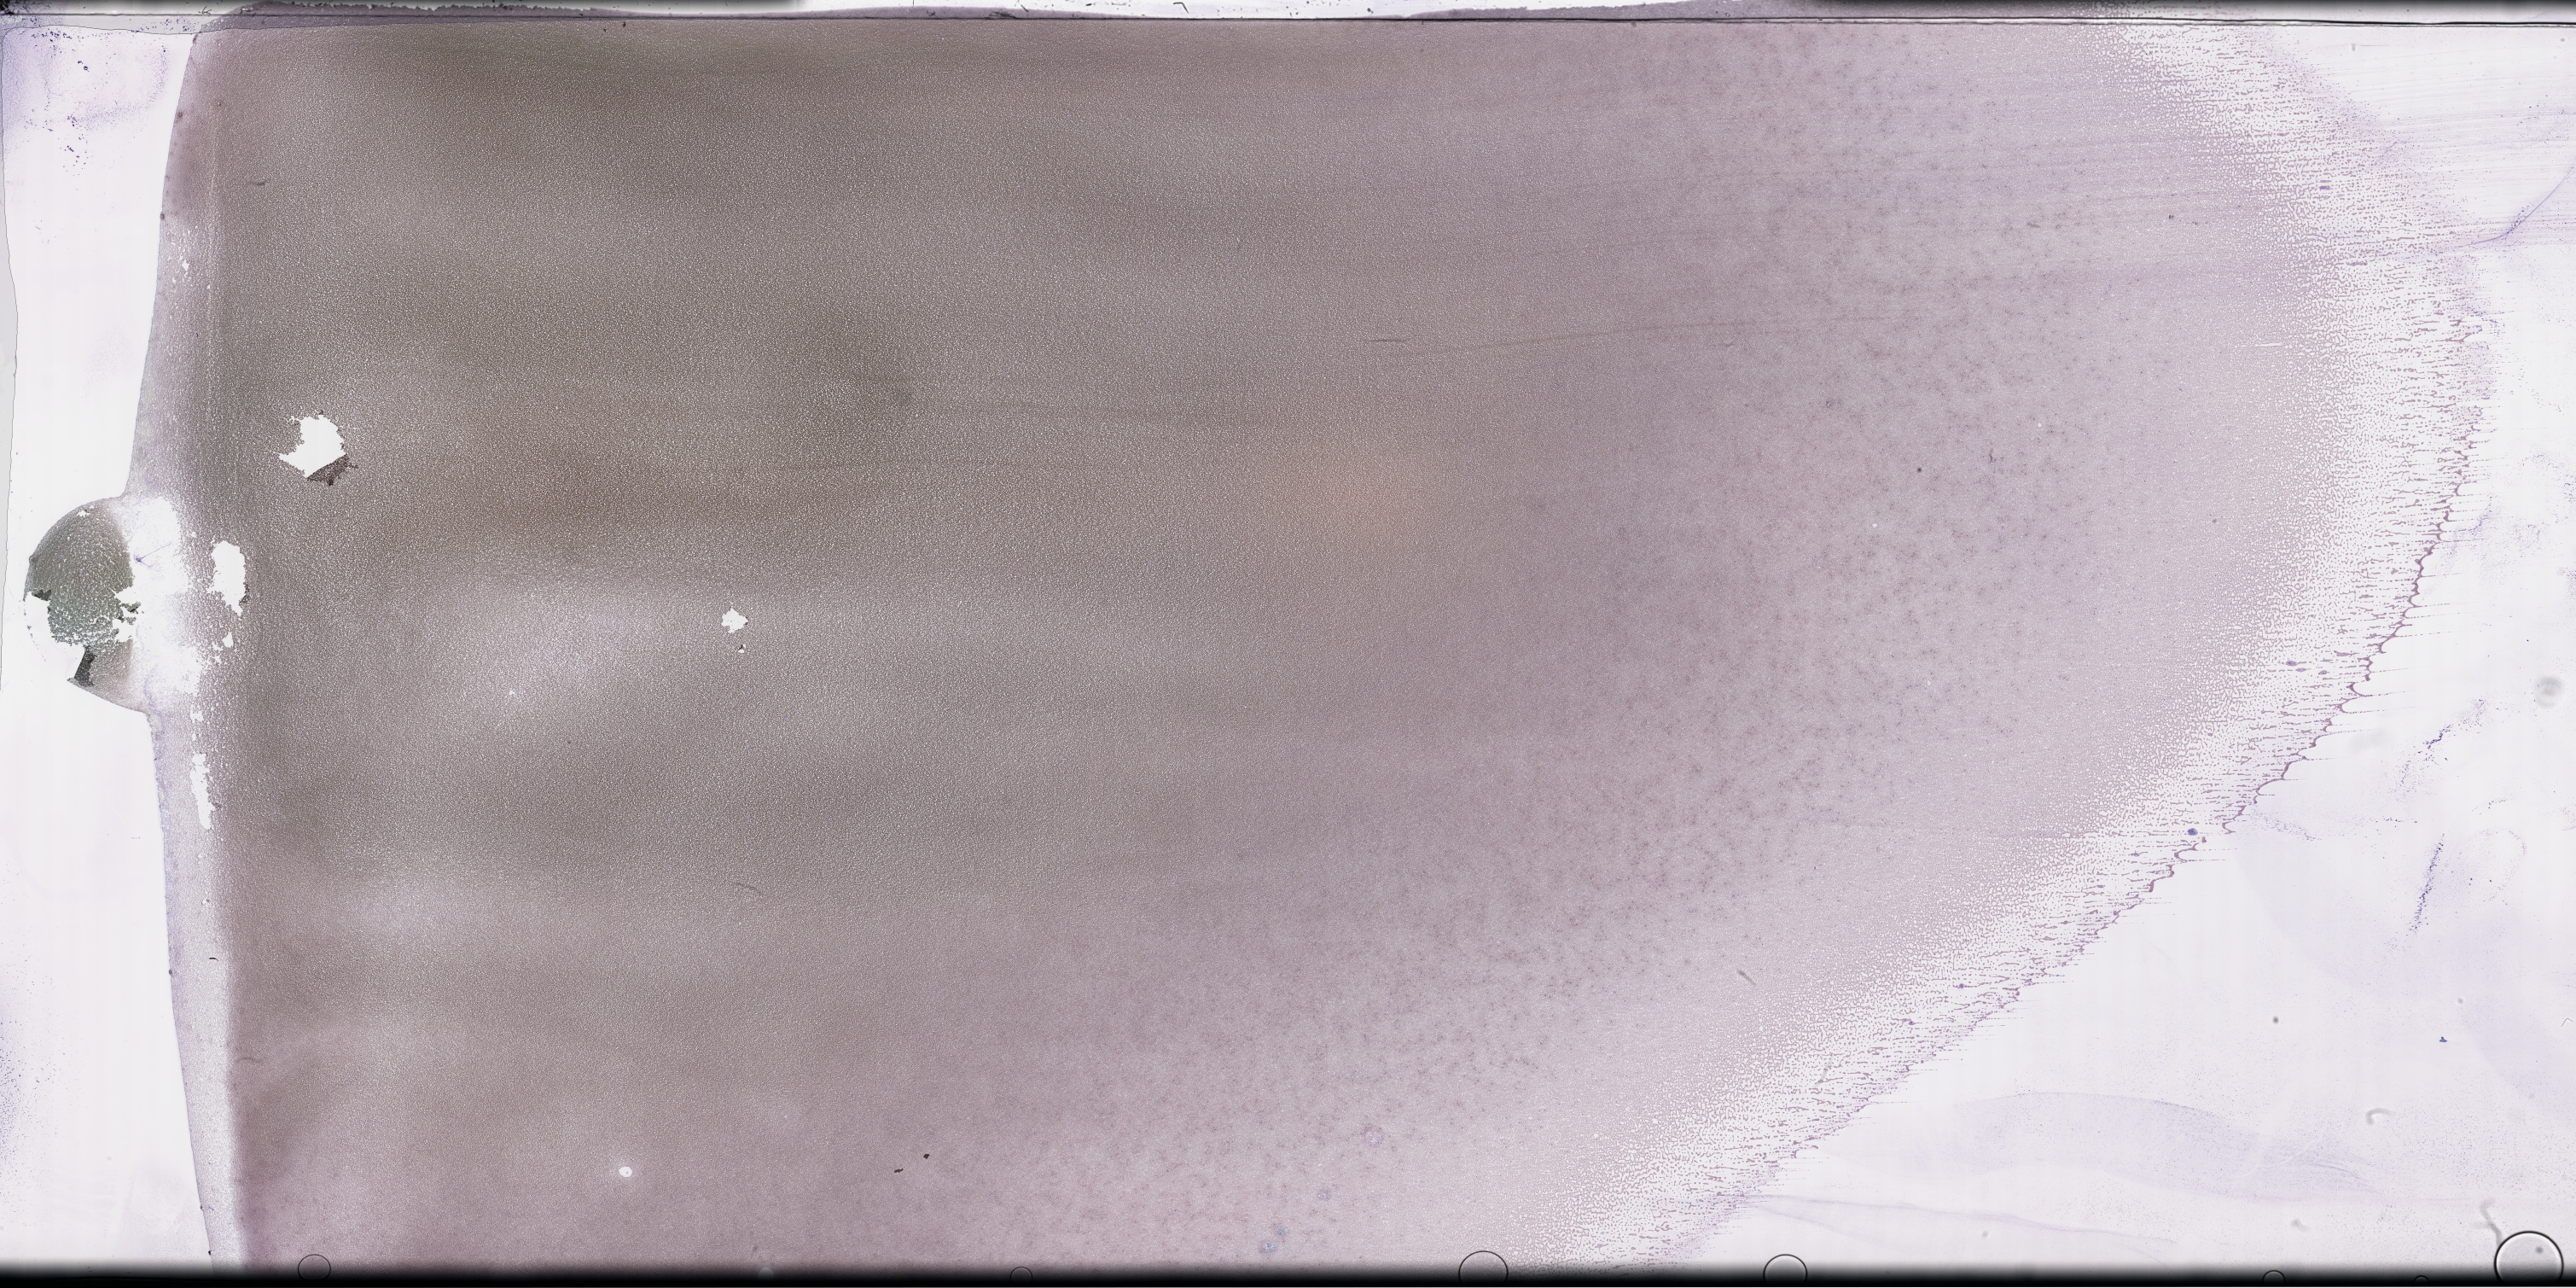
Whole-slide image of a whole blood smear, Wright-Giemsa stain — low-resolution overview of the scanned area, about 48.8 x 24.4 mm; EDTA-anticoagulated smear. Male patient.
From a patient with: Plasma Cell Myeloma.